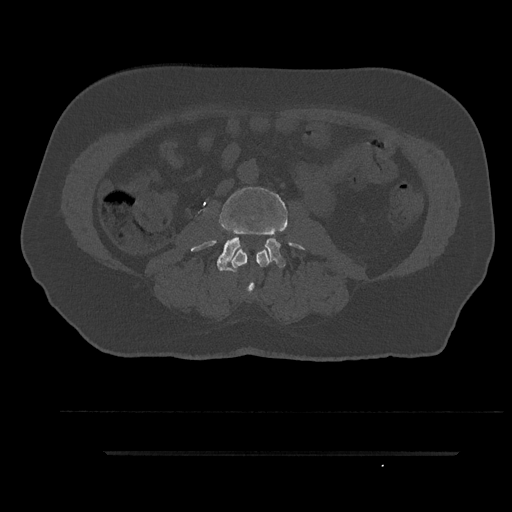
CT including the spine, one axial slice; position 66 of 797 along the scan axis; bone window (W 1800 / L 400 HU); 0.5 mm slice thickness; 512 × 512 image matrix, field of view 432 × 432 mm. Male patient, age 63 years. Case-level facts recorded for this patient, not image findings: primary cancer: renal; vertebrae with lytic lesions (as recorded): T8.
Outlined on this slice (semi-automatically segmented with operator editing):
- L2 vertebra: bounding box (x1, y1, x2, y2) in pixels: (232, 249, 269, 294)
- L3 vertebra: (190, 185, 304, 272)